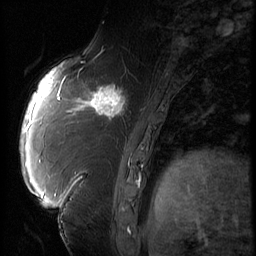
Breast MRI (dynamic contrast-enhanced), one sagittal slice; position 23 of 66 along the scan axis; 3 images stored at this slice position (order not interpretable as contrast timing); 1.5 T; TE 4.2 ms, TR 9 ms; 2.5 mm slice thickness; 256 × 256 image matrix, field of view 180 × 180 mm. Female patient, age 57 years. Case-level facts recorded for this patient, not image findings: setting: breast cancer imaged before/during neoadjuvant chemotherapy; receptor status: triple-negative.
Annotated regions visible in this slice (semi-automatically segmented with operator editing):
- analysis volume of interest (the breast-tissue region the enhancement analysis was run in; not a lesion): bounding box <86,74,138,129> (left, top, right, bottom; pixels)
- tumour enhancement mask (voxels above the 140 % enhancement threshold inside the analysis volume of interest): <86,81,128,122>